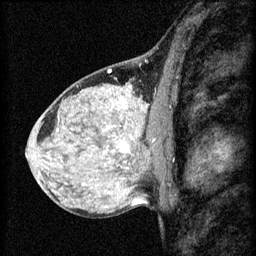
Breast MRI (dynamic contrast-enhanced), one sagittal slice. Position 35 of 60 along the scan axis. 3 images stored at this slice position (order not interpretable as contrast timing). 1.5 T. TE 4.2 ms, TR 8.2 ms. 2 mm slice thickness. 256 × 256 image matrix. Patient: female, 40 years.
Structures marked on this image (semi-automatically segmented with operator editing):
- analysis volume of interest (the breast-tissue region the enhancement analysis was run in; not a lesion): bounding box <108,108,167,159> (left, top, right, bottom; pixels)
- tumour enhancement mask (voxels above the 70 % enhancement threshold inside the analysis volume of interest): <120,134,155,153>